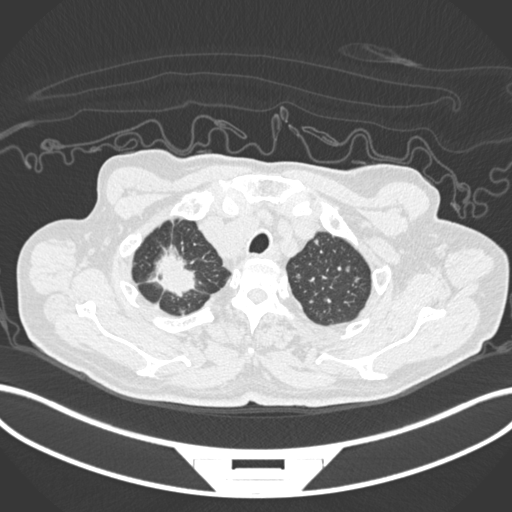
Chest CT, one axial slice. Position 193 of 207 along the scan axis. Lung window (W 1500 / L -600 HU). 1 mm slice thickness. 512 × 512 image matrix. Male patient, age 69 years. Case-level facts recorded for this patient, not image findings: clinical TNM (as recorded): T1c N1 M1.
Outlined on this slice (rectangle marked by the reading radiologist):
- lung tumour (recorded histology: adenocarcinoma): bounding box [x1, y1, x2, y2] px = [150, 244, 201, 299]